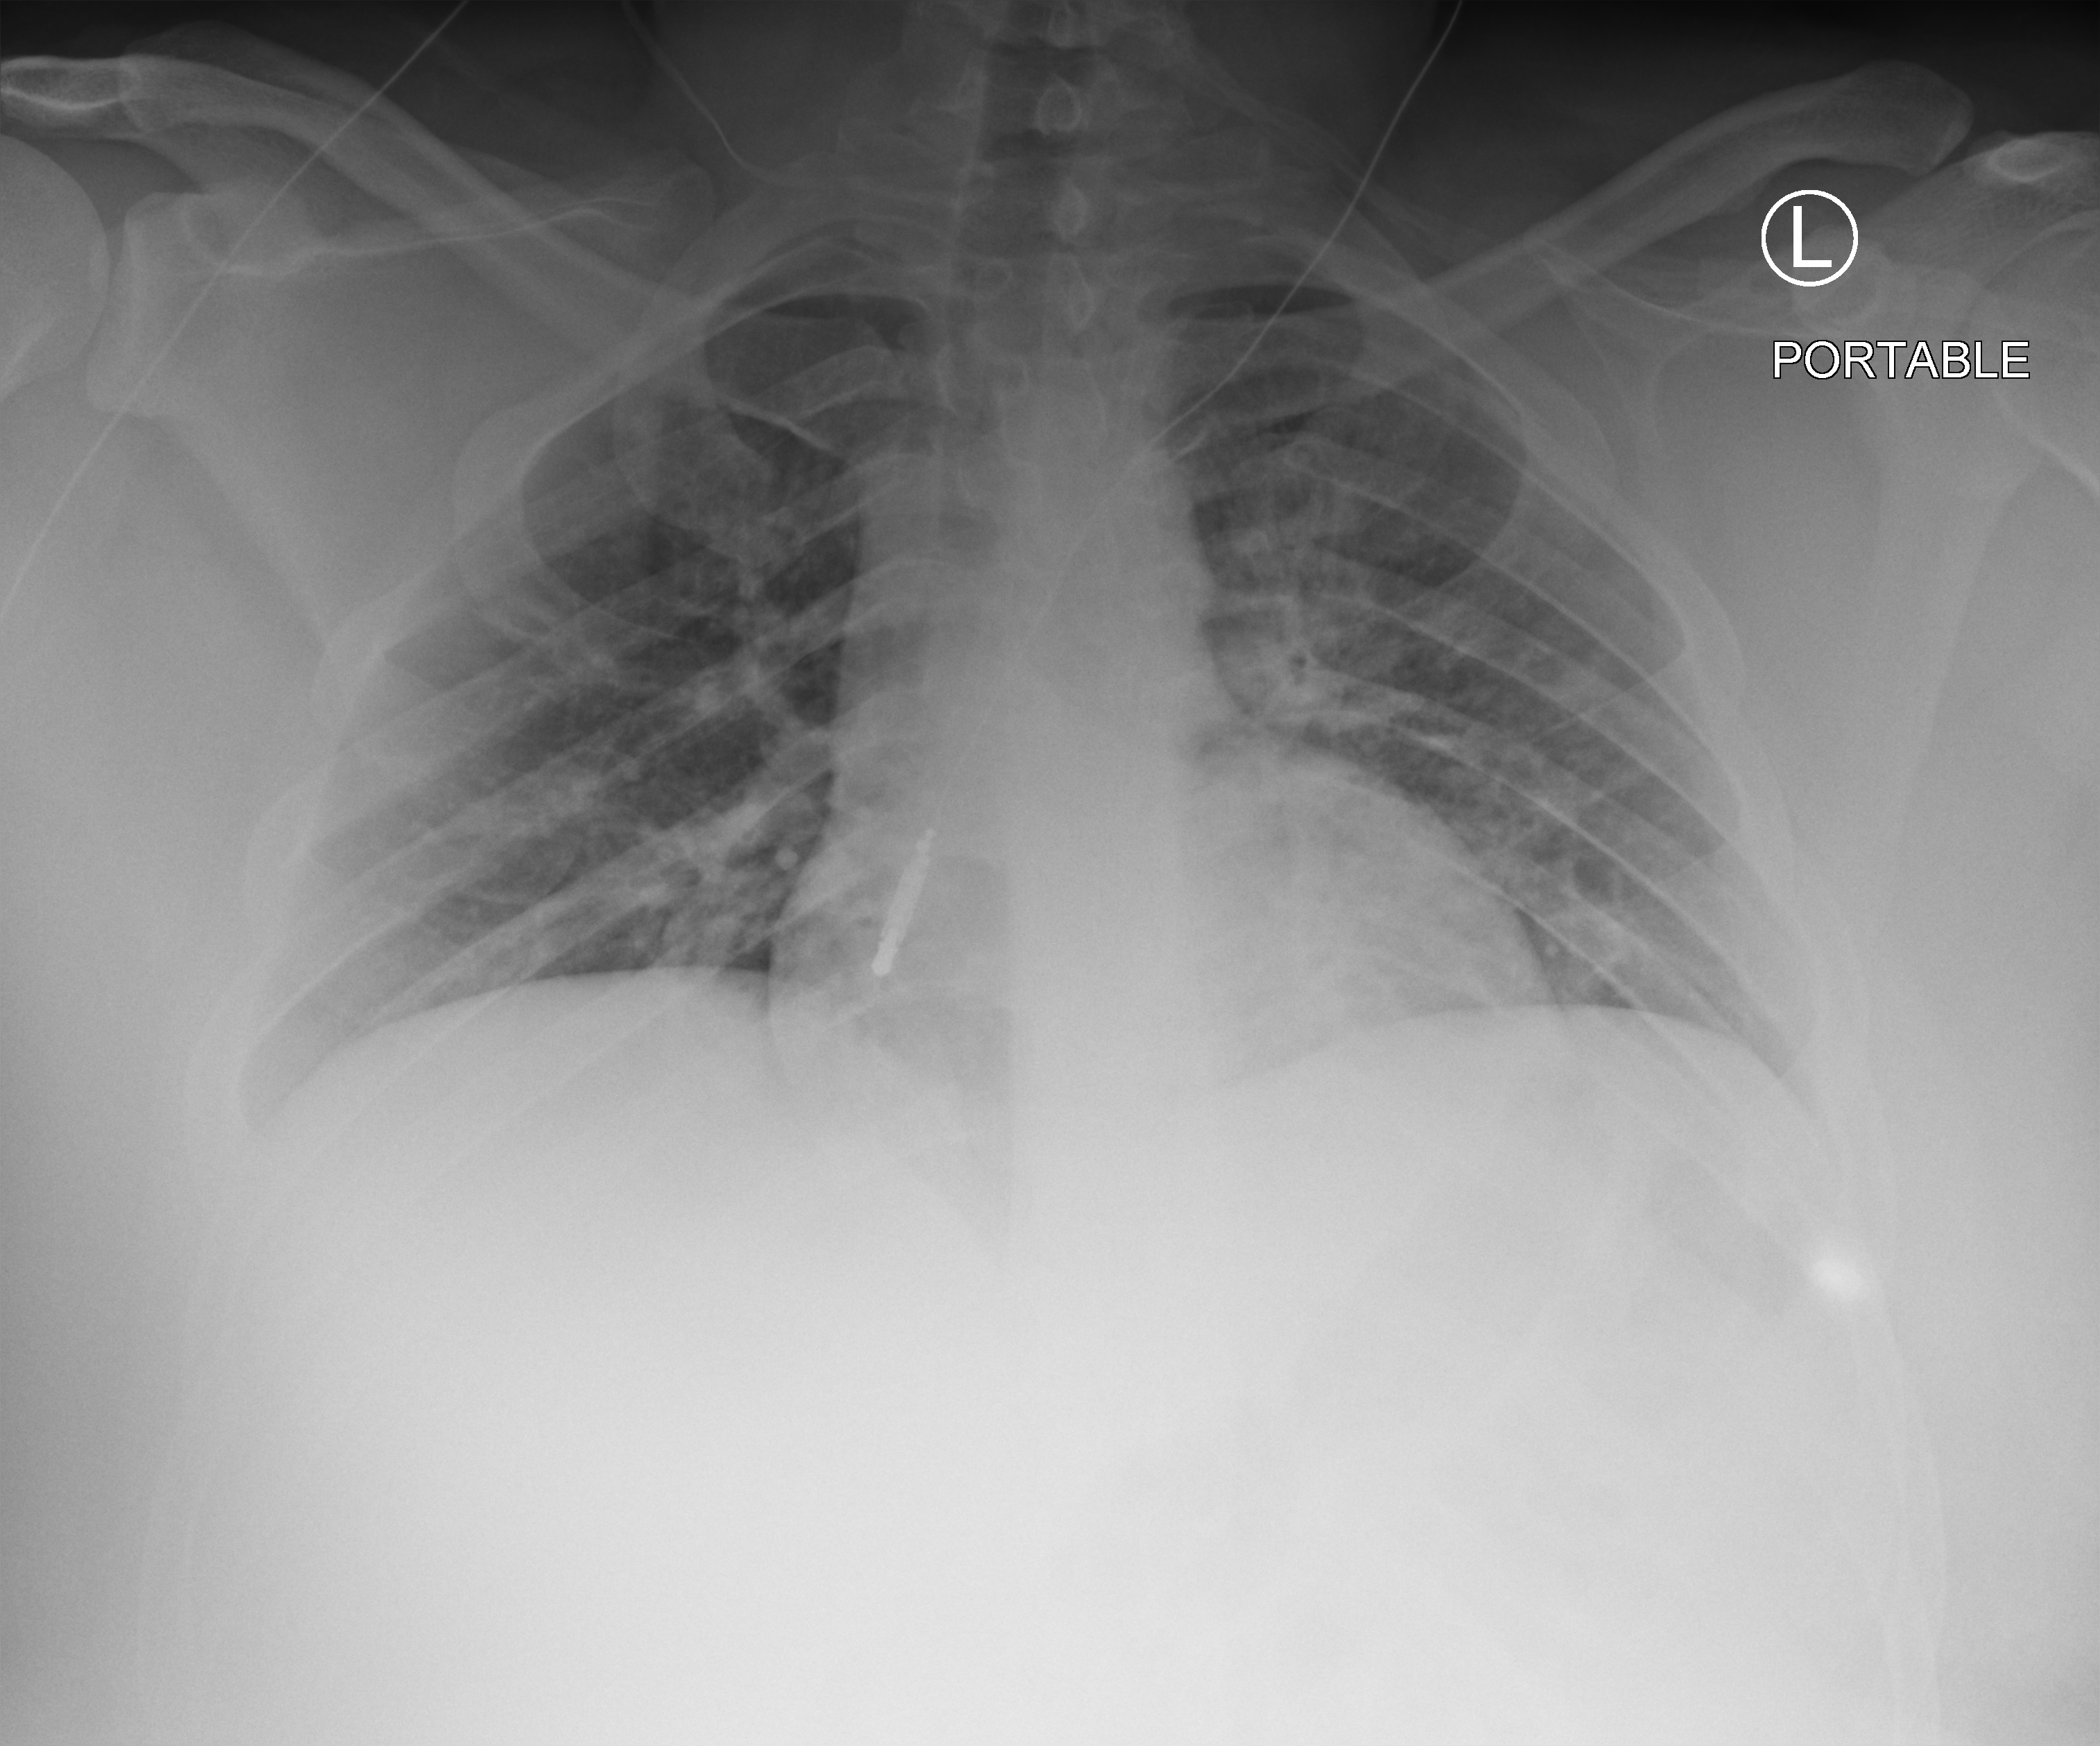
Portable chest radiograph; anteroposterior (AP) projection. Patient hospitalised with COVID-19; male, aged 18–59 years.
Admission-level facts for this patient (not findings on this image; timing relative to this image not recorded): length of hospital stay: 12 days.